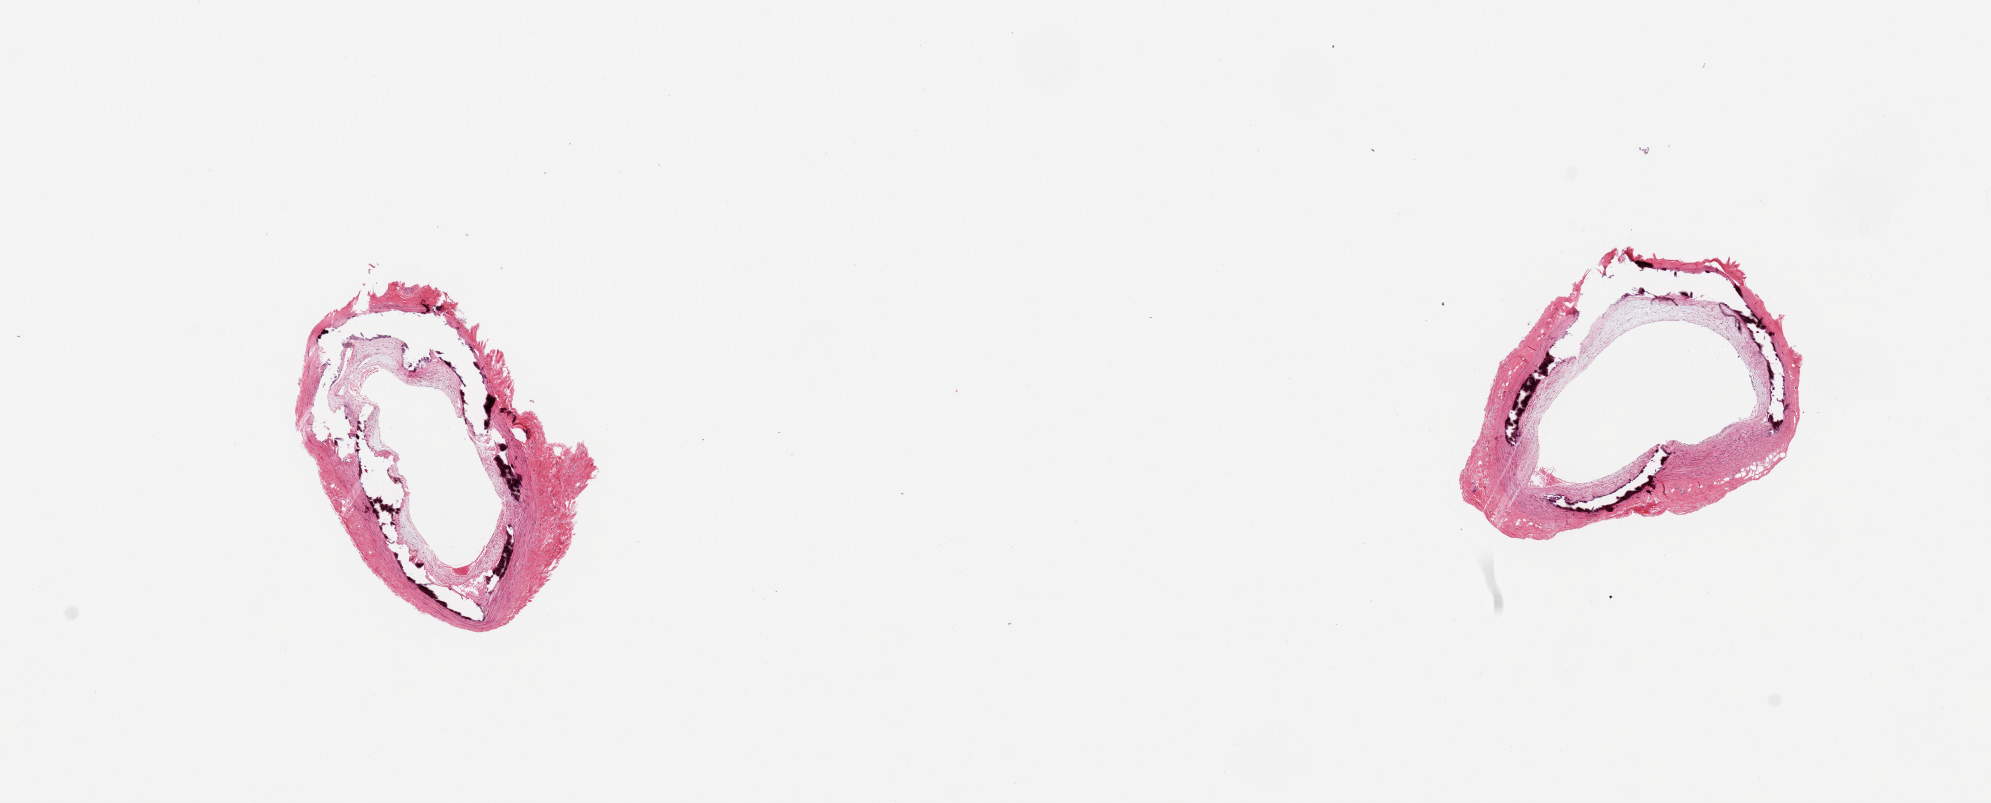
Whole-slide image, H&E stain, shown as a low-resolution overview of the whole scanned area (about 15.8 x 6.4 mm), PAXgene-fixed, paraffin-embedded tissue, section of tibial artery (target tissue), donor tissue sample. Male donor.
• review note (as recorded): 2 pieces; atherosclerosis, medial calcific sclerosis